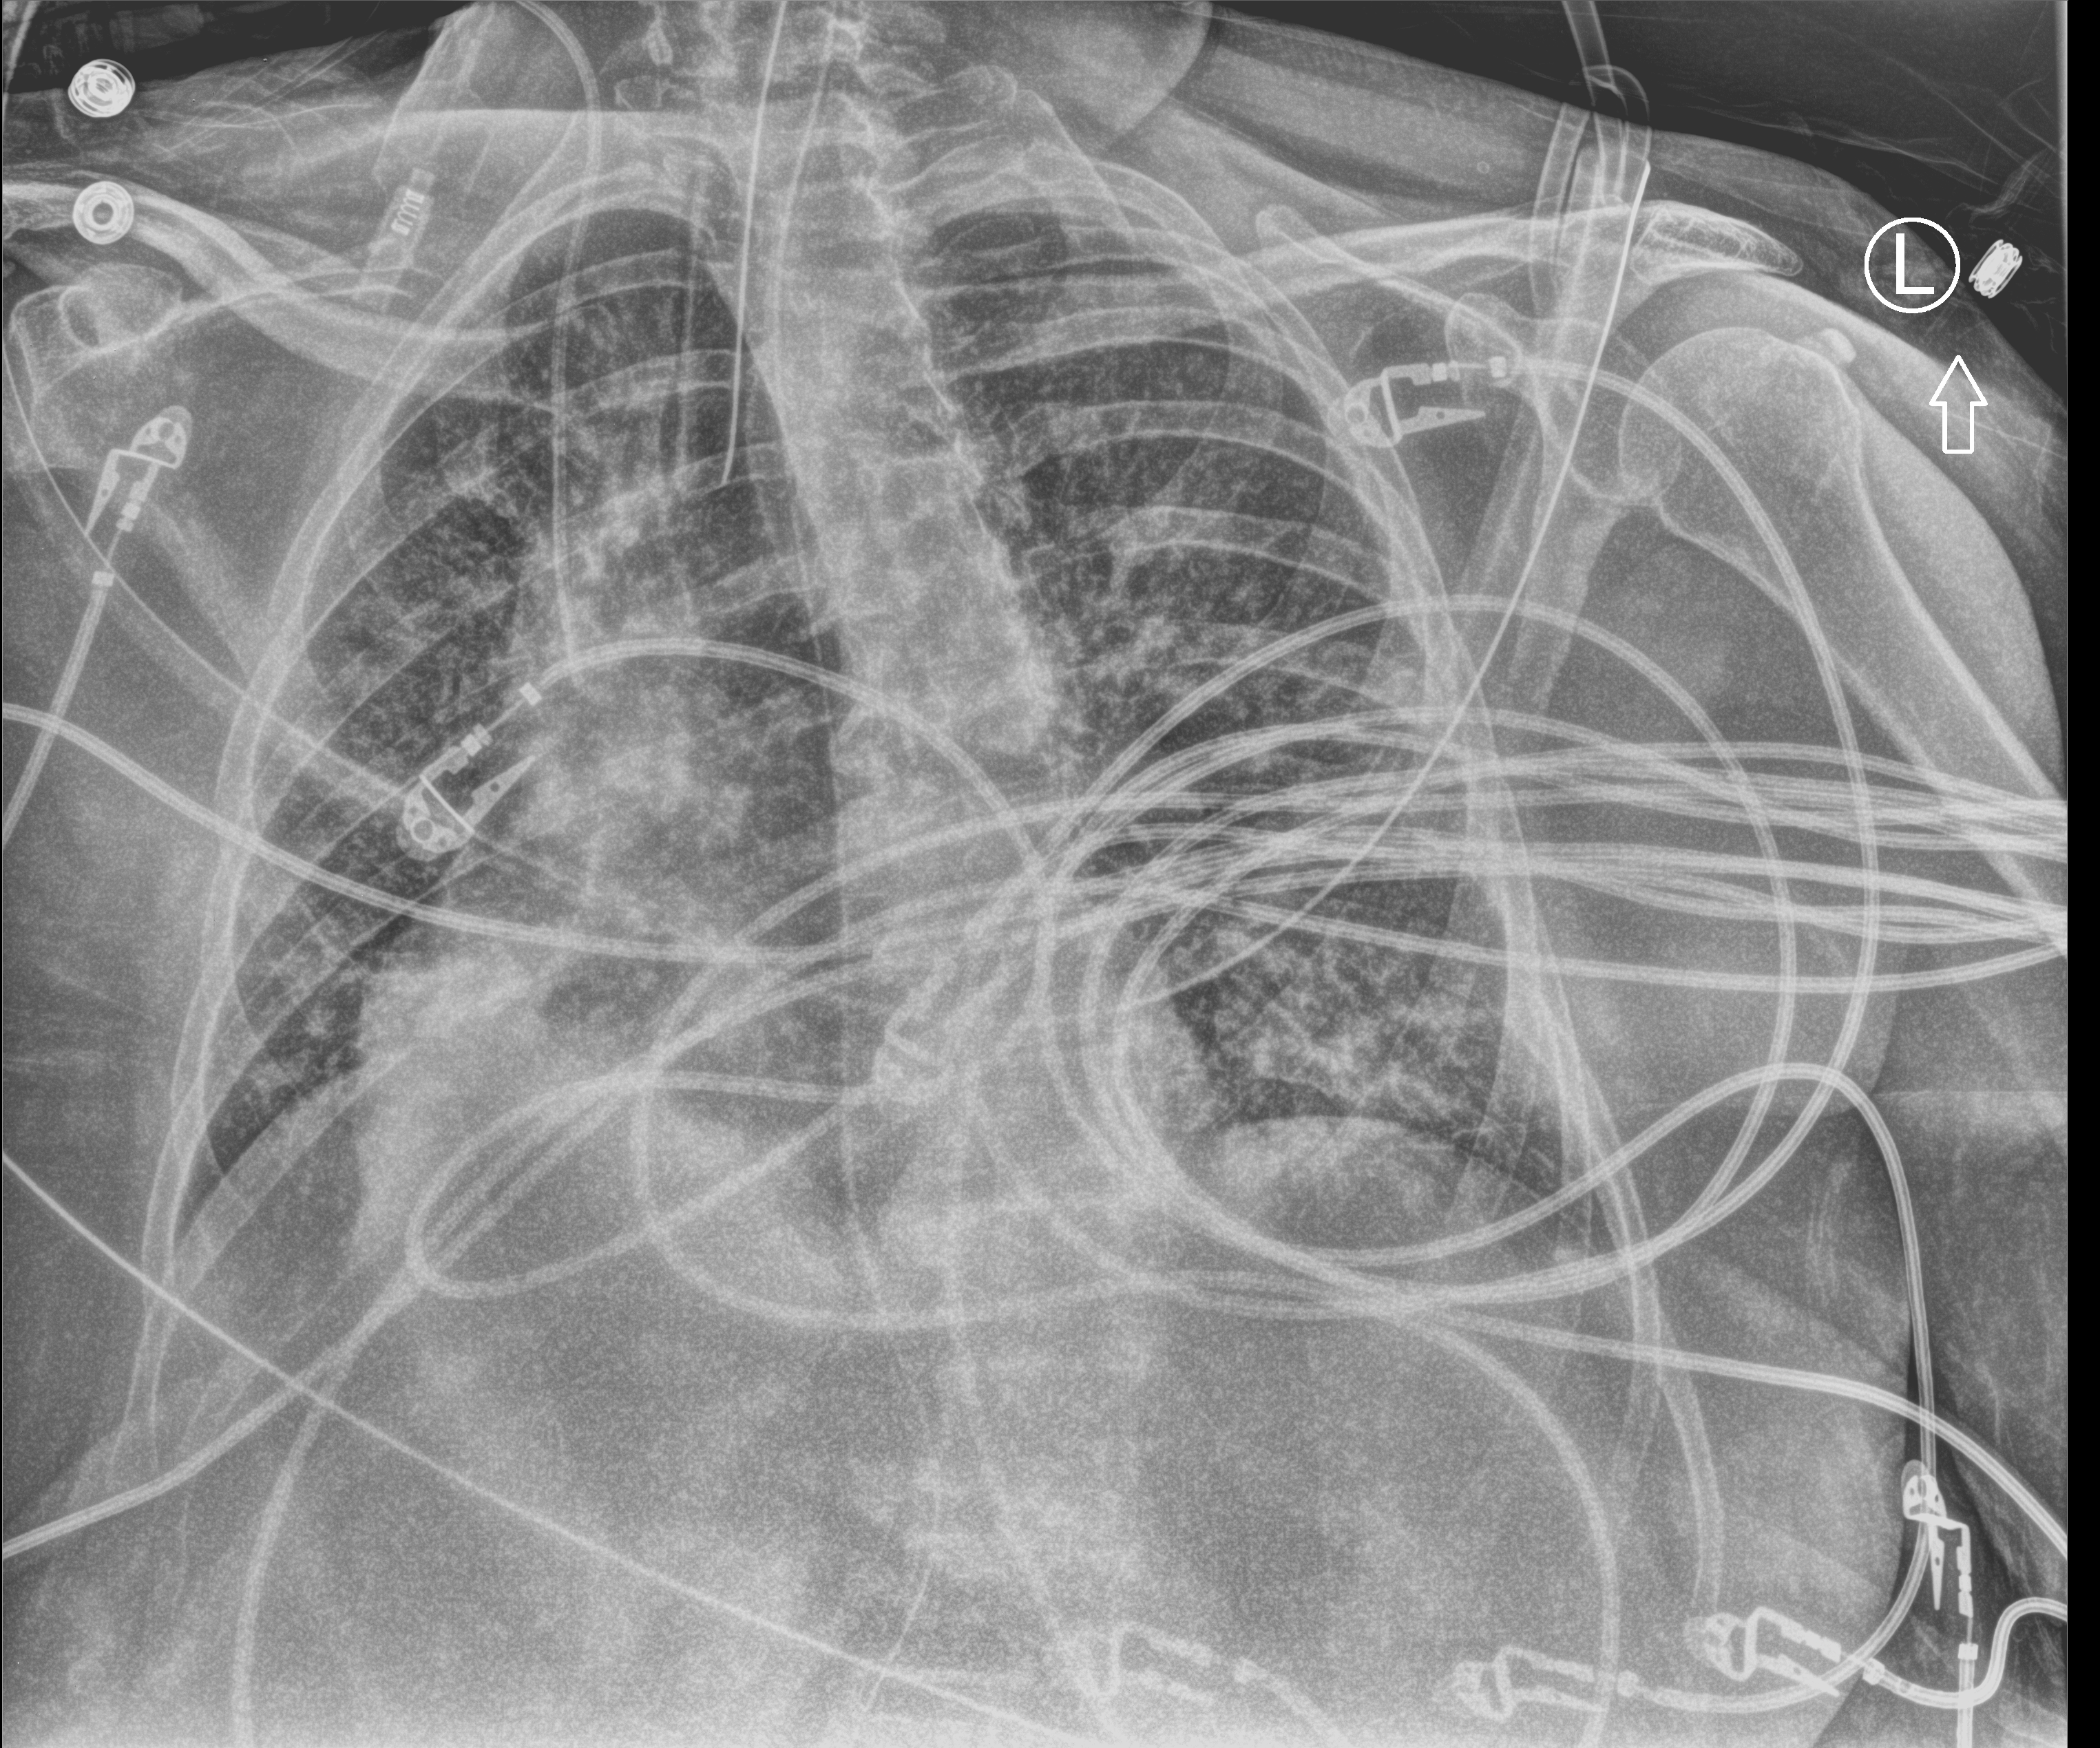
Chest X-ray (portable), anteroposterior (AP) projection. Patient hospitalised with COVID-19; female, aged 75–90 years.
From the hospital-stay record, not from the radiograph (when in the stay this image was taken is not recorded): mechanically ventilated during this hospital stay: yes; diabetes (admission record): no; length of hospital stay: 31 days.